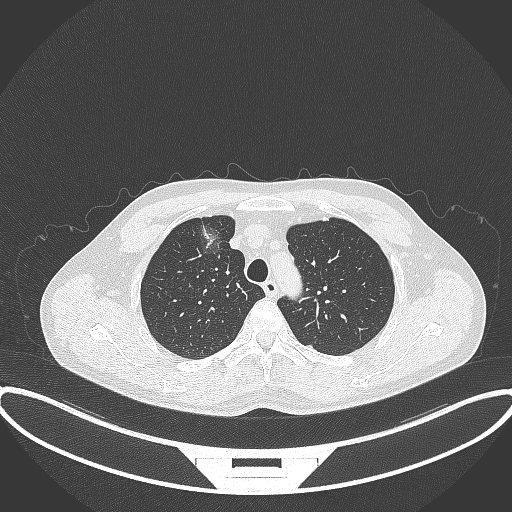
Chest CT, one axial slice; 120 kVp; lung window (W 1500 / L -600 HU); 1 mm slice thickness; 512 × 512 image matrix, field of view 424 × 424 mm. Patient: male, 60 years. Case-level facts recorded for this patient, not image findings: clinical TNM (as recorded): T1c N0 M0.
Structures marked on this image (rectangle marked by the reading radiologist):
- lung tumour (recorded histology: adenocarcinoma): bounding box (x1, y1, x2, y2) in pixels: (191, 213, 230, 264)